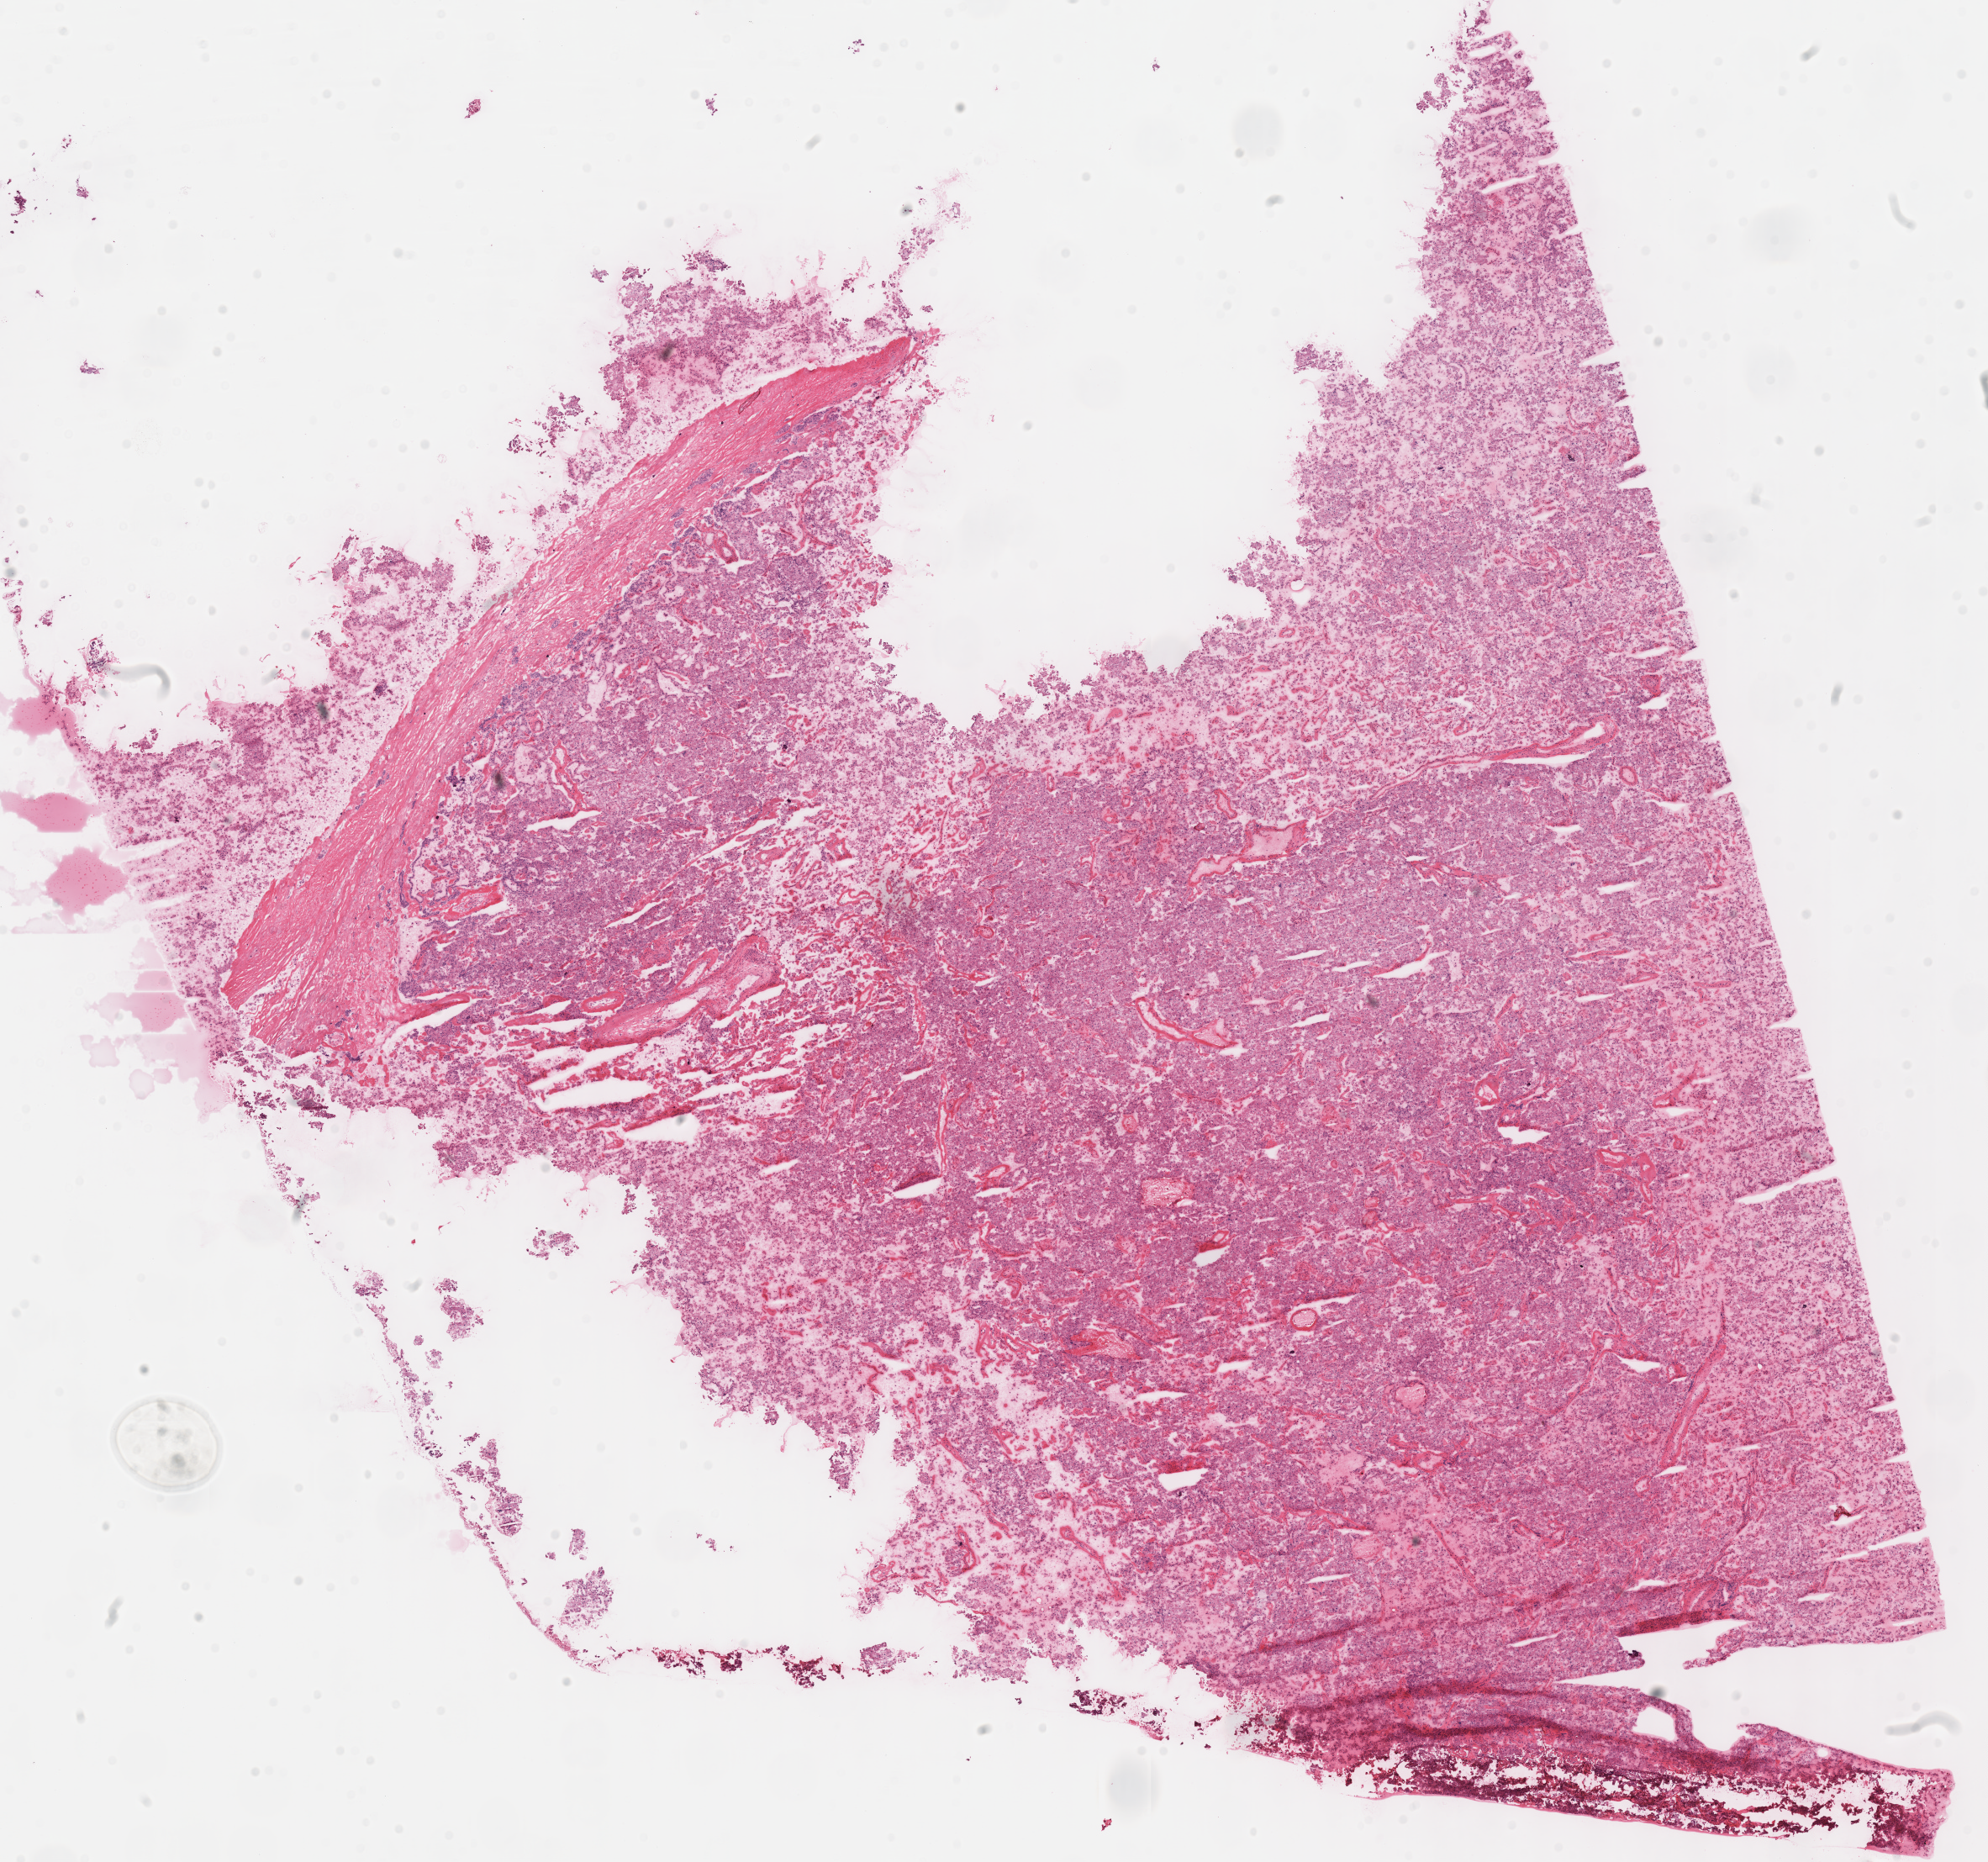
Whole-slide histology image, H&E-stained — whole scanned area (about 18.6 x 17.4 mm, acquisition: 40x scan) shown as a low-resolution overview, frozen section from the top of the tissue portion, kidney, primary tumour sample. Female, age 37 years at initial diagnosis. Pathologist review of this section (percent, as recorded): tumour cells 94%, tumour nuclei 90%, normal cells 0%, stromal cells 6%, necrosis 0%. Inflammatory infiltration, as recorded: lymphocyte infiltration 2%, monocyte infiltration 0%, neutrophil infiltration 0%.
Histologic diagnosis: Renal cell carcinoma, chromophobe type. Lymph nodes positive (case pathology): 0 of 6 examined. AJCC pathologic stage: III (6th edition). Laterality: left. TNM: T3a N0 M0.